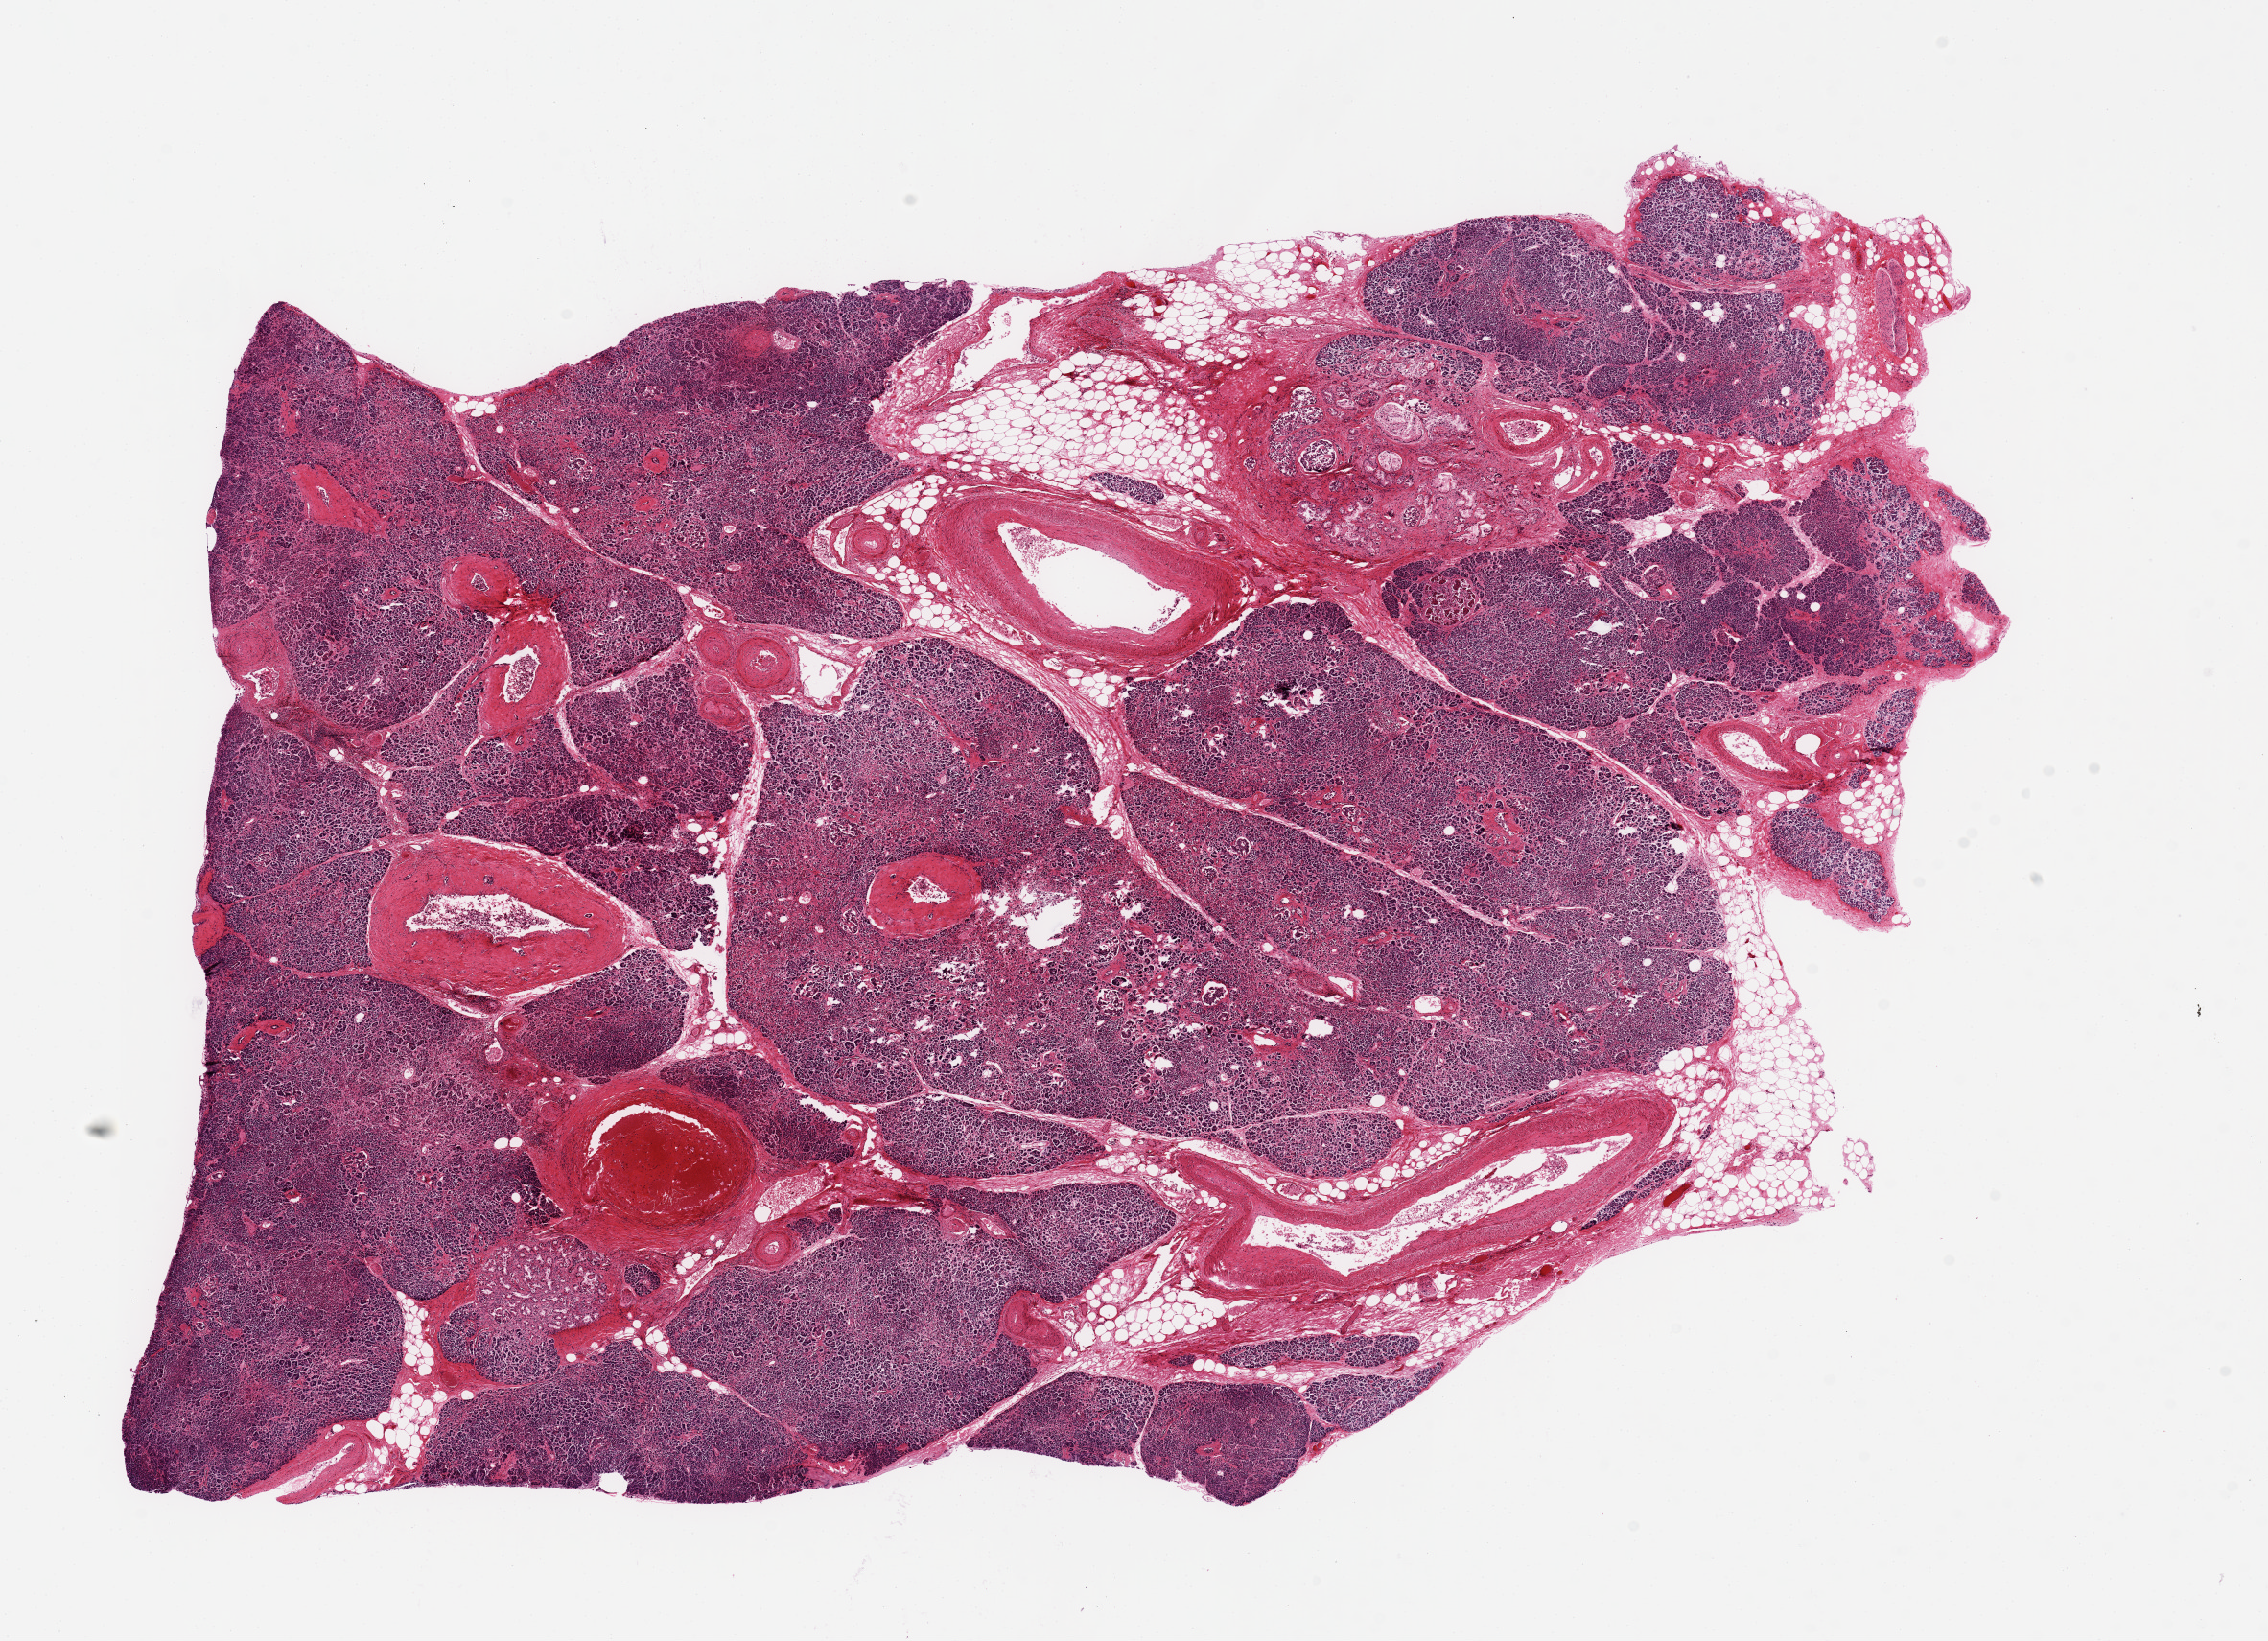
Haematoxylin and eosin whole-slide image, low-resolution overview of the scanned area, about 18.7 x 13.5 mm, PAXgene-fixed, paraffin-embedded tissue, sampled site (target tissue): pancreas, donor tissue sample. Donor sex: male.
- reviewer comment on this tissue sample: Moderate autolysis & peripancreatic saponification